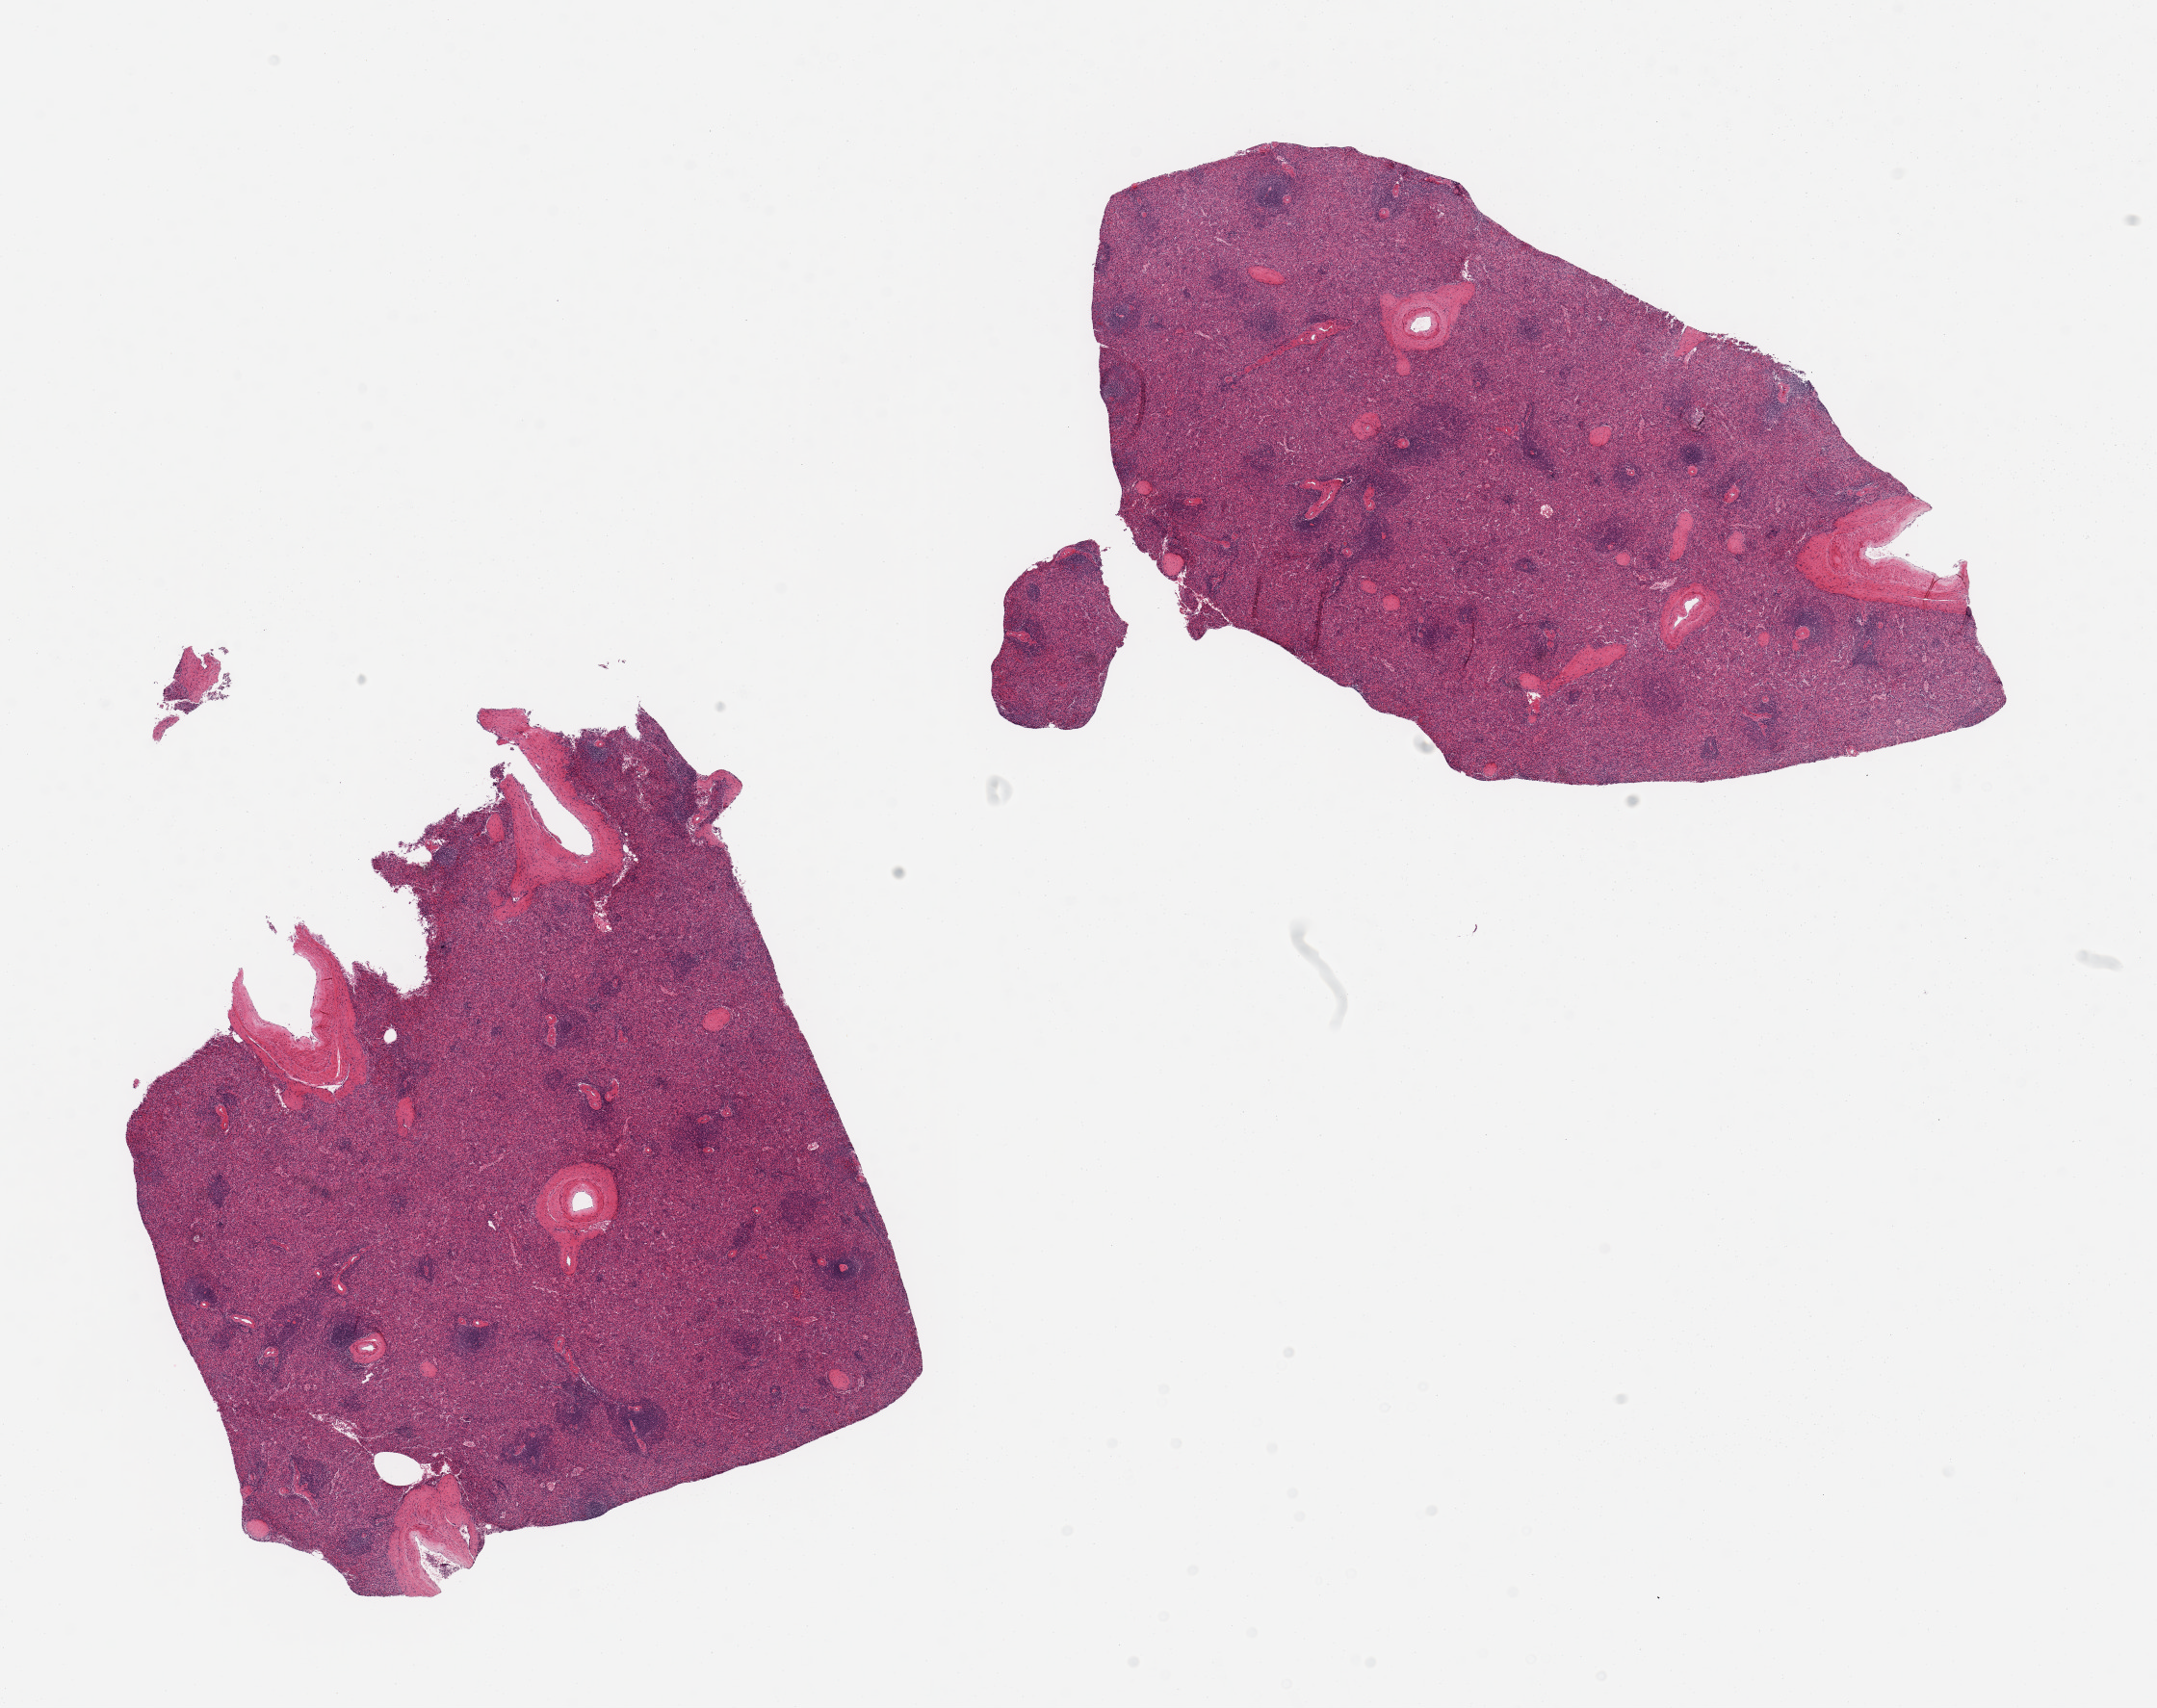
Whole-slide image, hematoxylin and eosin (H&E) stain, a low-resolution overview of the entire scanned area, about 17.7 x 14.0 mm, PAXgene-fixed paraffin-embedded (PFPE) section, sampled site (target tissue): spleen, donor tissue sample. Male donor.
Review note (as recorded): 2 pieces, moderate congestion.